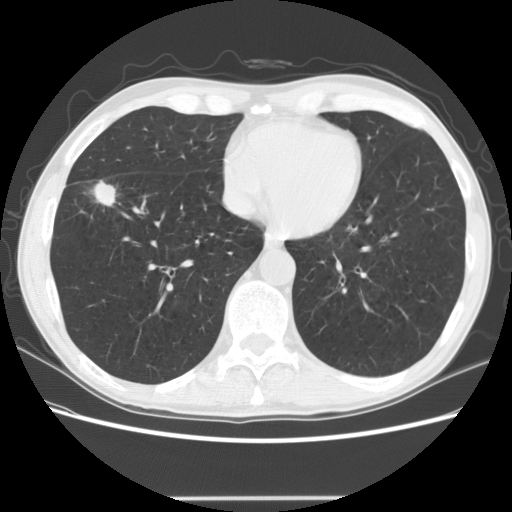
Low-dose screening chest CT, one axial slice. Slice 52 of 145 in the series (ordered by position). 140 kVp. Lung window (W 1500 / L -600 HU). 2.5 mm slice thickness. 512 × 512 image matrix, field of view 365 × 365 mm.
Outlined on this slice (outlined manually by an expert reader):
- lesion 1 (tumor, middle lobe of right lung): bounding box <90,180,120,207> (left, top, right, bottom; pixels)